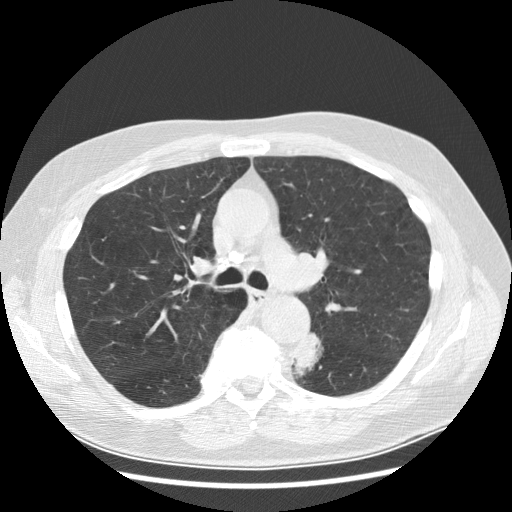
Chest CT (low-dose screening protocol), one axial image, baseline screening round, lung window (W 1500 / L -600 HU), standard (soft-tissue) reconstruction kernel (STANDARD), 120 kVp. Male participant, aged 70 years at enrolment.
Expert reader's lesion annotation, bounding box [x1, y1, x2, y2] px = [277, 335, 326, 380]. Reader record for this screening exam (exam-level; its link to the box is not recorded): non-calcified nodule or mass ≥4 mm, left lower lobe, 27 × 16 mm, spiculated (stellate) margins, soft tissue attenuation, pre-existing on the prior screen: yes; interval growth: yes.